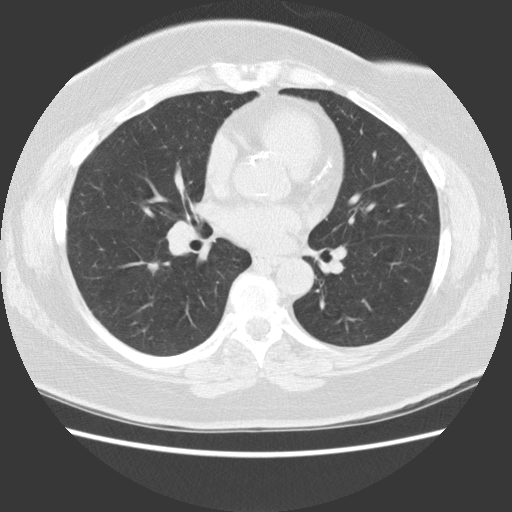
Chest CT (low-dose screening protocol), one axial image; baseline screening round; lung window (W 1500 / L -600 HU); 2.5 mm slice thickness; standard (soft-tissue) reconstruction kernel (STANDARD); 512 × 512 image matrix, field of view 350 × 350 mm. Female participant, aged 62 years at enrolment. Former smoker at enrolment.
Expert-annotated lung lesion, bounding box (x1, y1, x2, y2) in pixels: (115, 238, 175, 294). Reader record for this screening exam (exam-level; its link to the box is not recorded): non-calcified nodule or mass ≥4 mm, right lower lobe, 12 × 10 mm, spiculated (stellate) margins, soft tissue attenuation. Official screen result: positive, change unspecified: nodule(s) >= 4 mm or enlarging nodule(s), mass(es), or other non-specific abnormalities suspicious for lung cancer. Later outcome: lung cancer diagnosed 182 days after this screen — large cell carcinoma, NOS, right lower lobe, moderately differentiated (G2), stage IA (AJCC 6th edition), 22 mm at pathology.